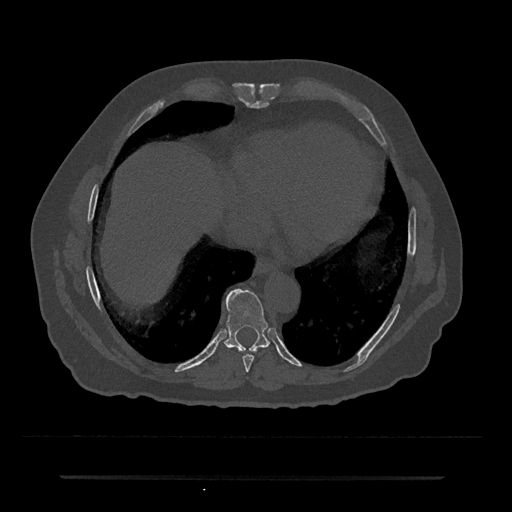
CT including the spine, one axial slice. Position 295 of 797 along the scan axis. 120 kVp. Bone window (W 1800 / L 400 HU). 512 × 512 image matrix, field of view 437 × 437 mm. Male patient, age 69 years. From the clinical record (not read from this slice): primary cancer: prostate.
Structures marked on this image (semi-automatically segmented with operator editing):
- T8 vertebra: bounding box (x1, y1, x2, y2) in pixels: (242, 354, 254, 372)
- T9 vertebra: (224, 289, 270, 352)